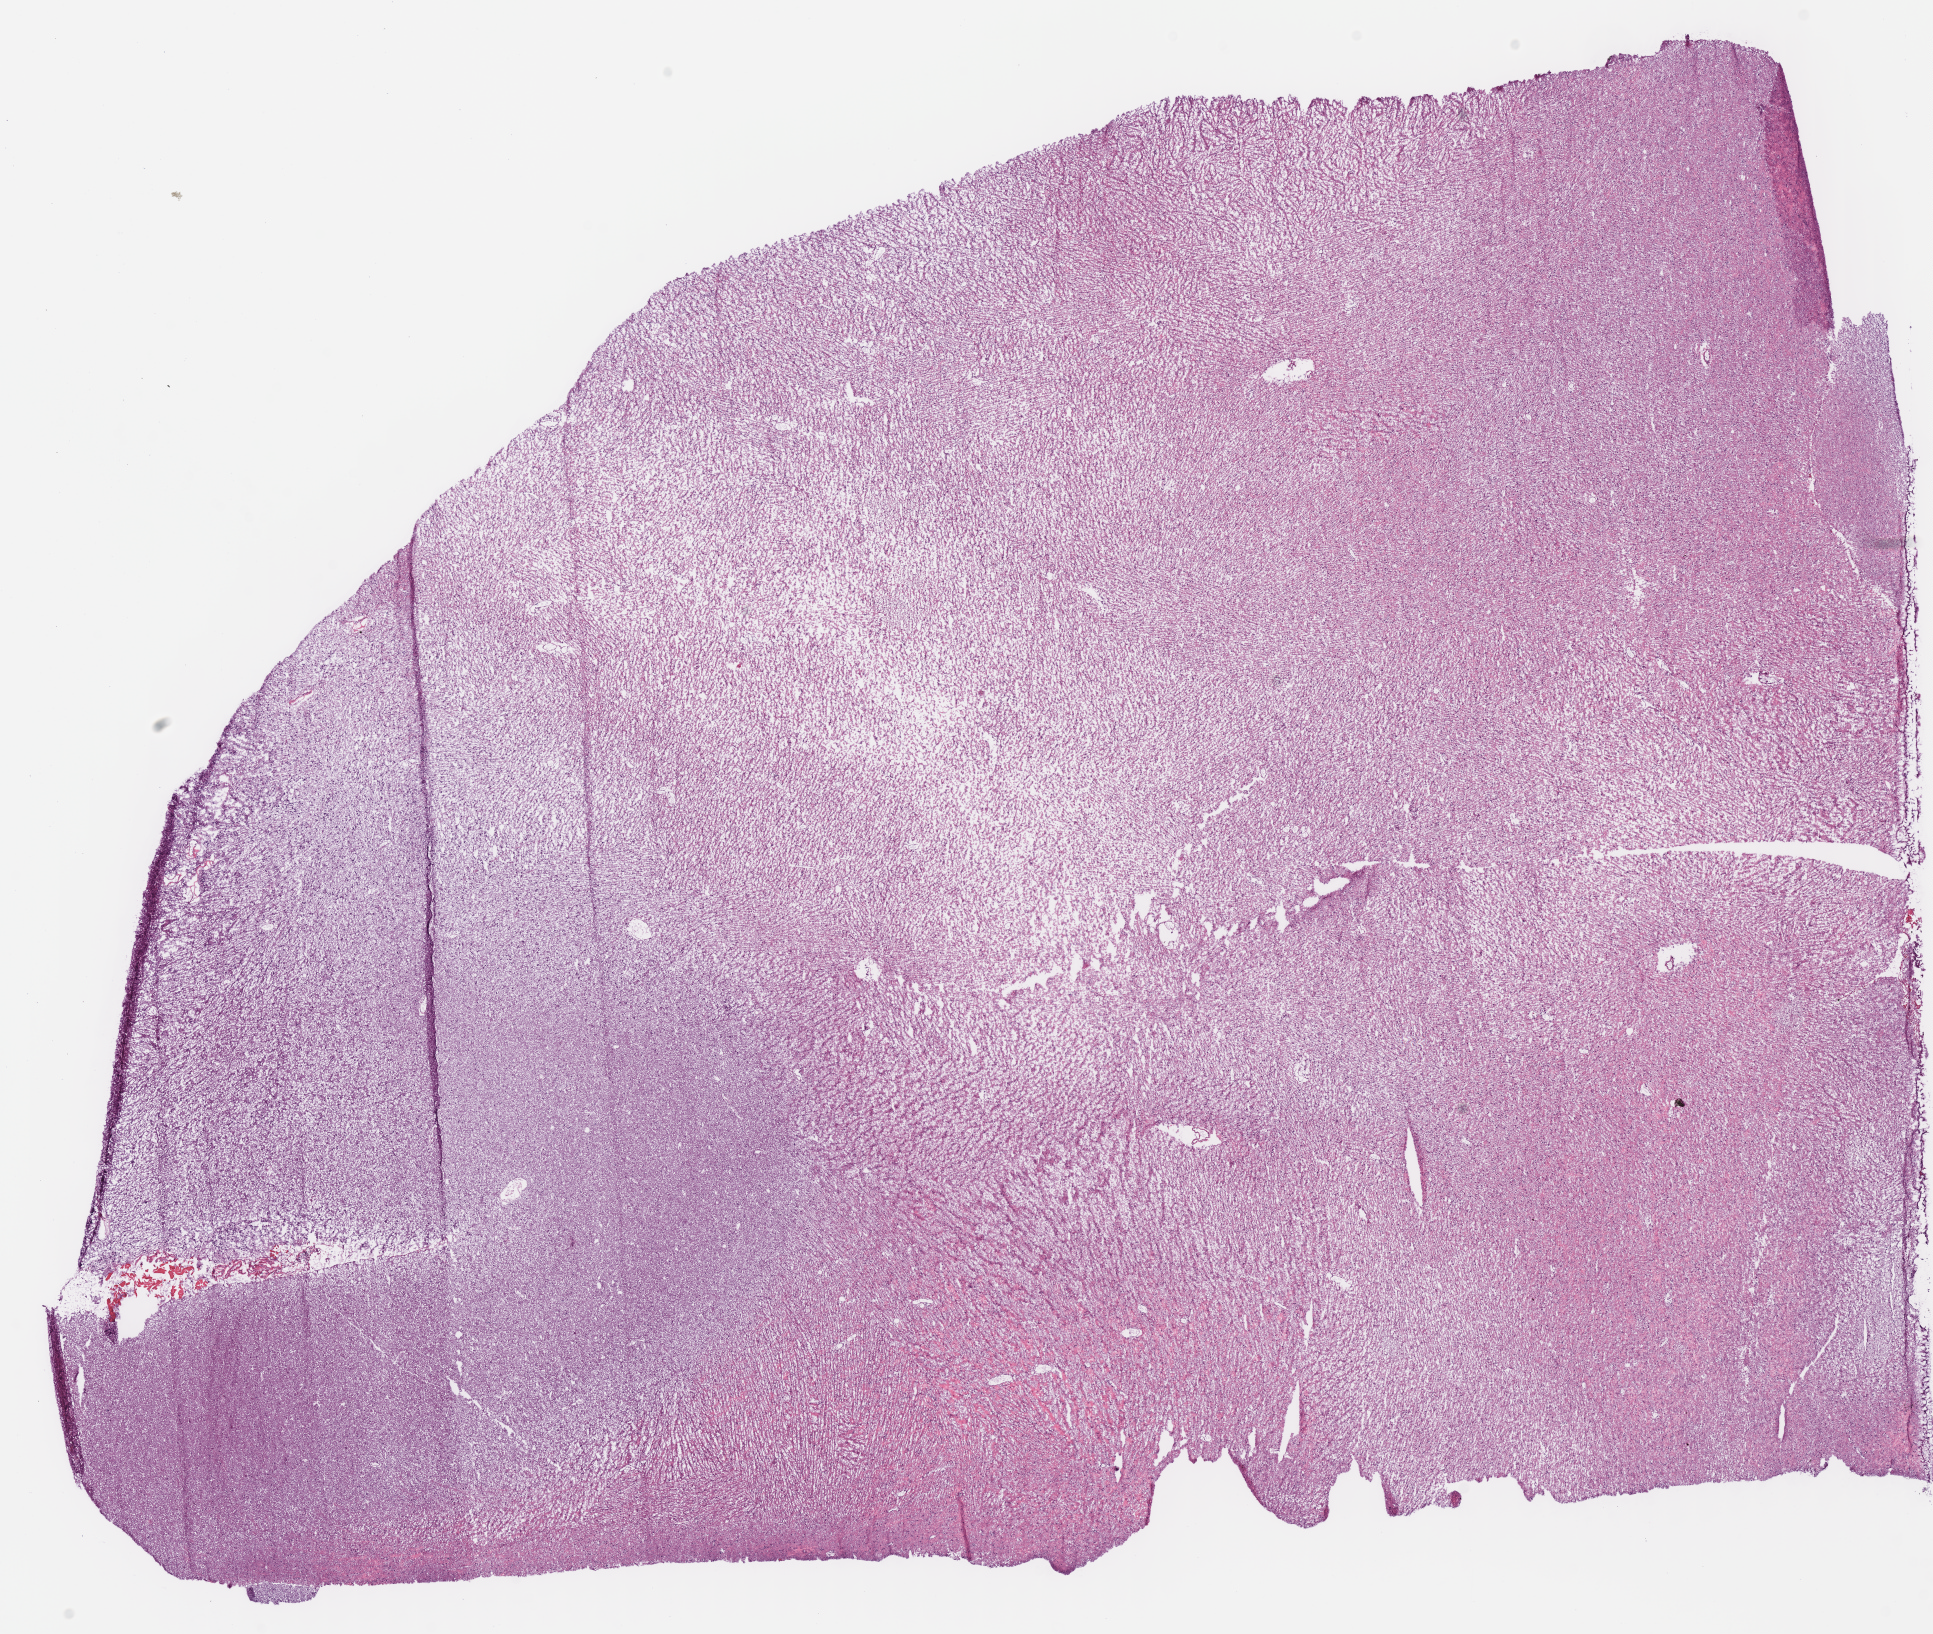
Digitized H&E-stained tissue section (whole slide) — shown as a low-resolution overview of the whole scanned area (about 15.2 x 12.9 mm, acquisition: 40x scan); frozen section from the bottom of the tissue portion; primary tumour sample from the brain. Patient: female, age at initial diagnosis 45 years. Histologic grade: G2 (moderately differentiated). Composition of this section per pathologist review: tumour cells 100%, tumour nuclei 65%, normal cells 0%, stromal cells 0%, necrosis 0%.
Laterality: right. Histologic diagnosis: Oligodendroglioma, NOS (cerebrum).